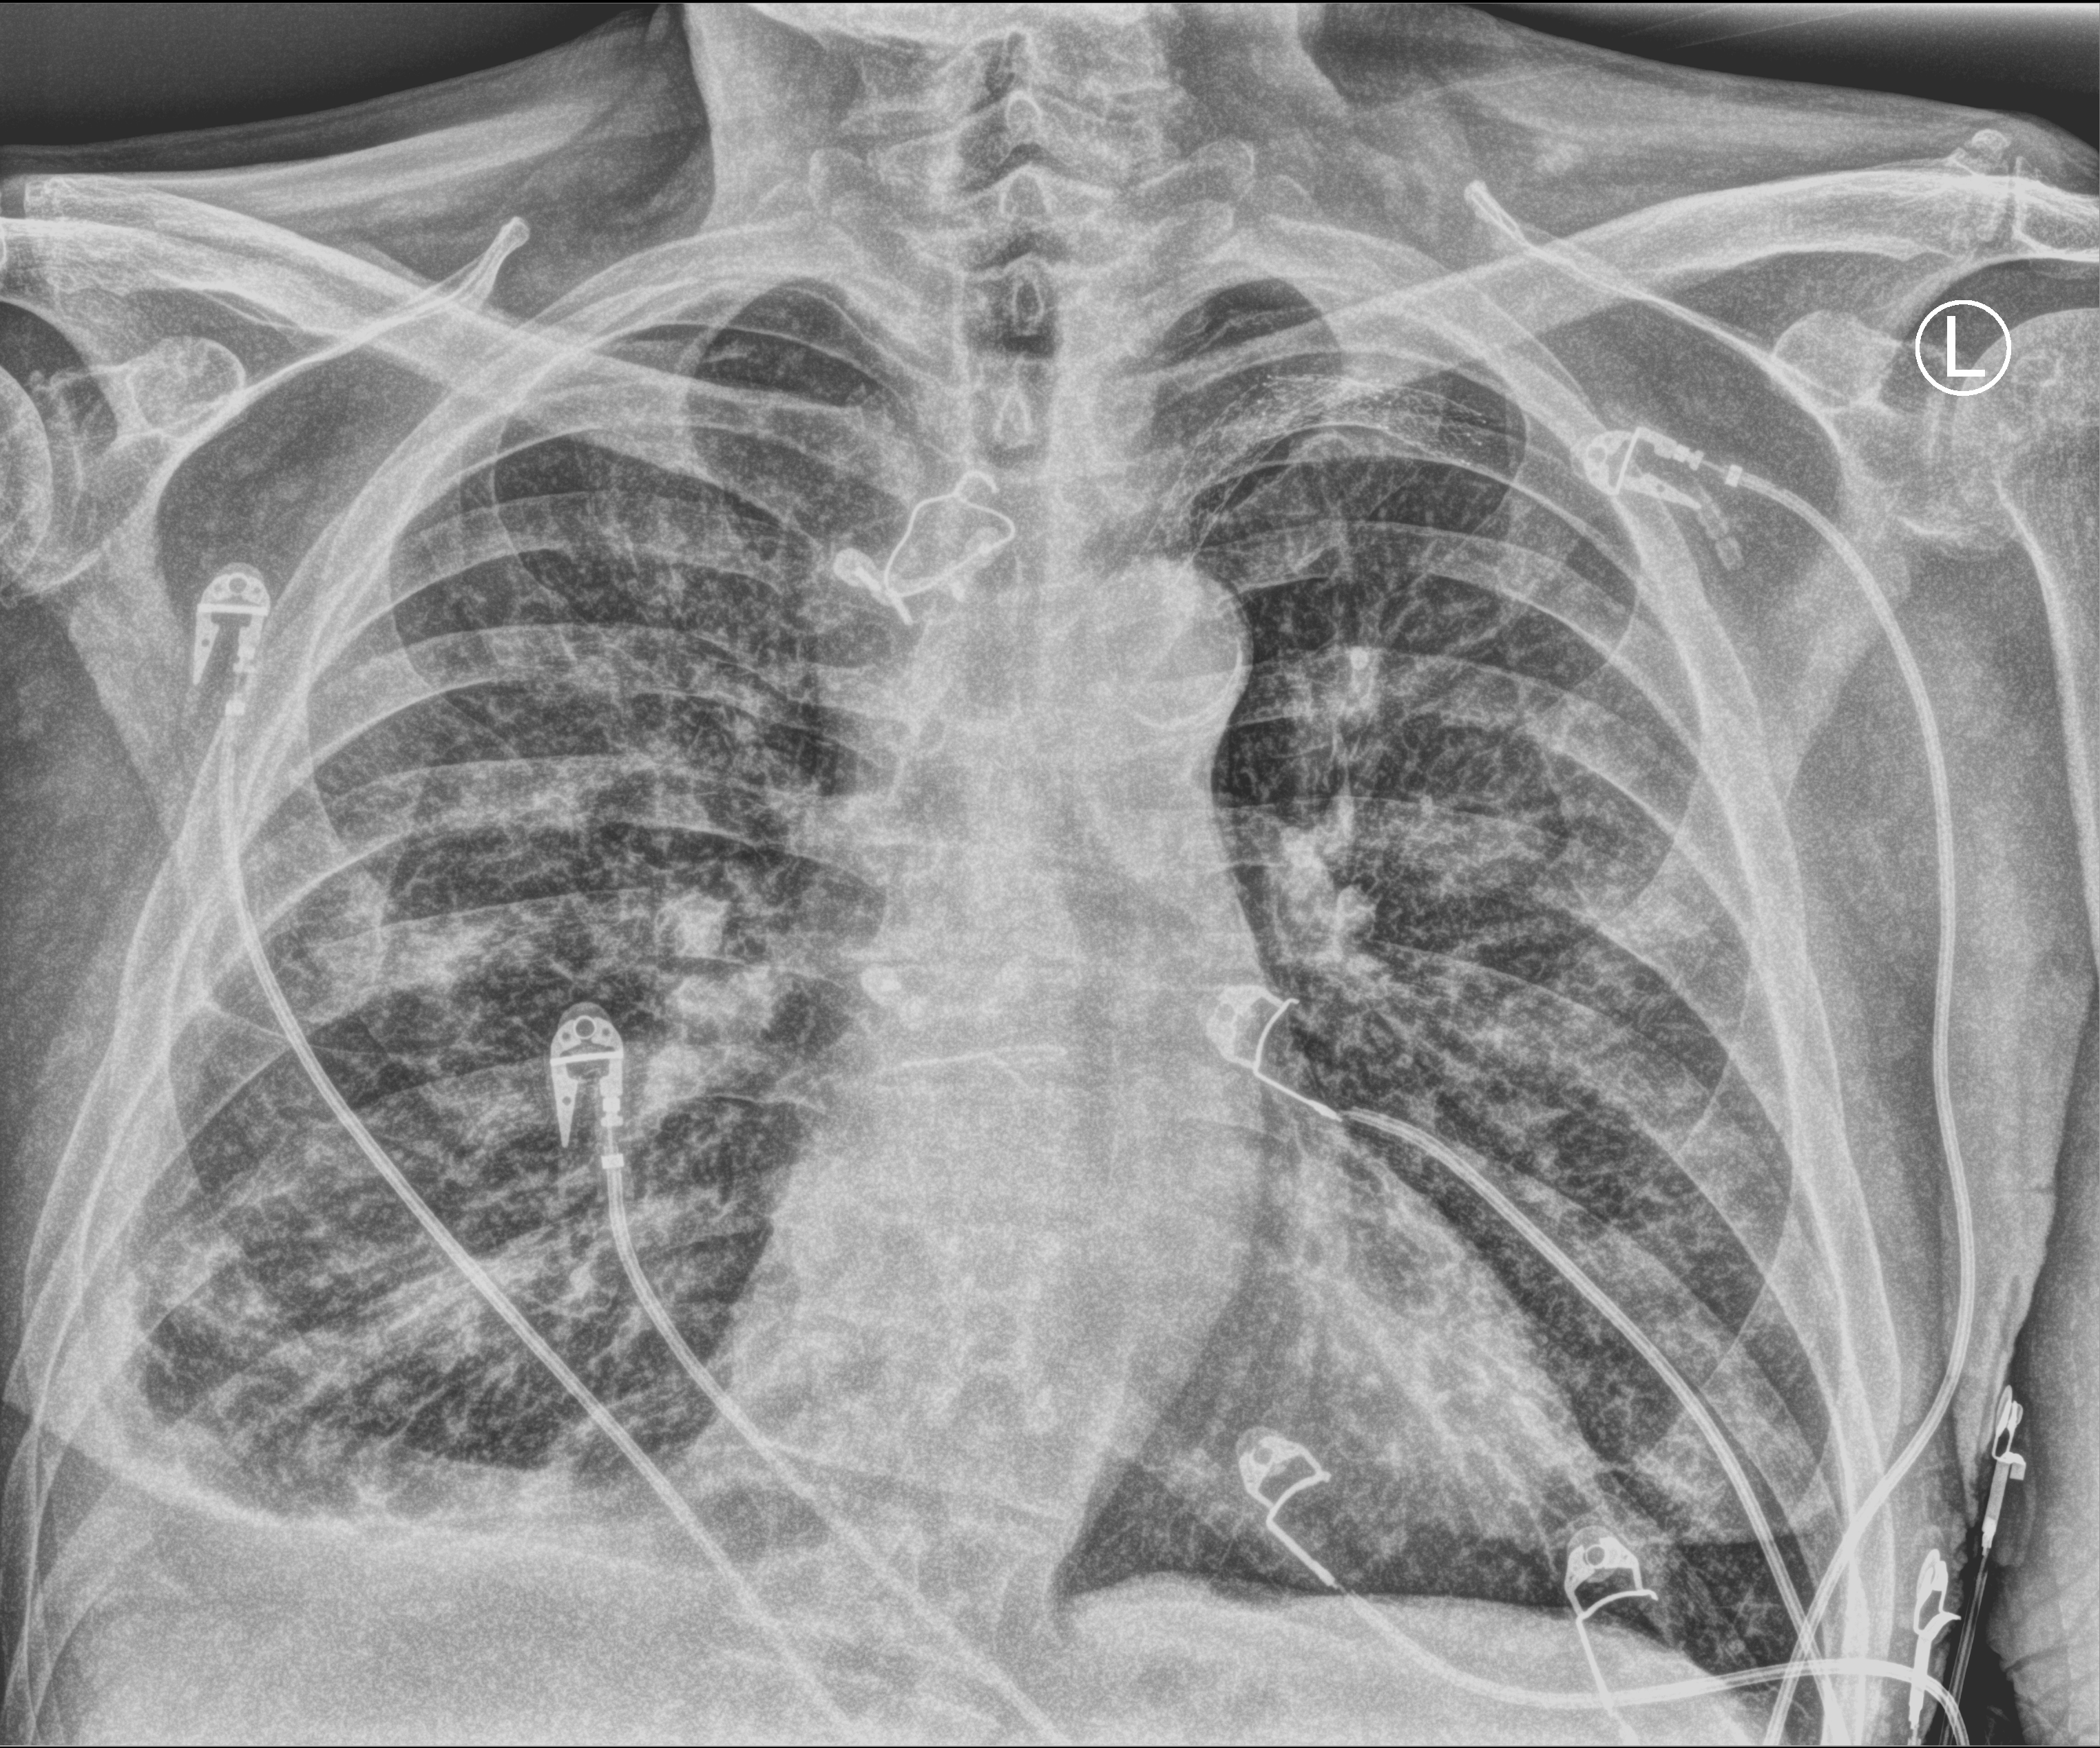
Bedside chest radiograph (computed radiography); anteroposterior (AP) projection. Male patient hospitalised with COVID-19, age 75–90 years.
Hospital-stay facts (about this admission, not read from this image; timing relative to this image not recorded): mechanically ventilated during this hospital stay: no; admitted to intensive care during this hospital stay: no.